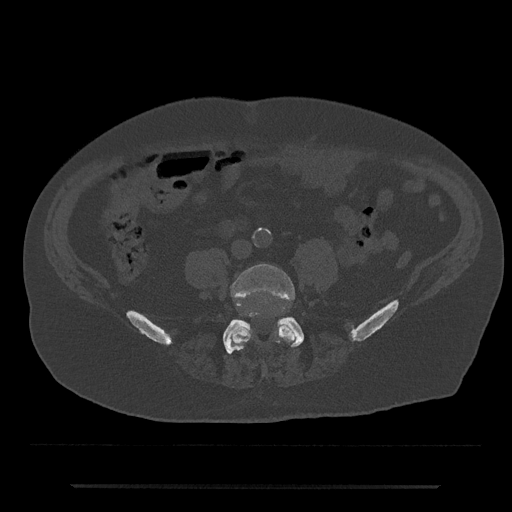
CT including the spine, one axial slice; position 319 of 797 along the scan axis; reconstruction kernel Br40s/3; bone window (W 1800 / L 400 HU); 0.5 mm slice thickness; 512 × 512 image matrix, field of view 434 × 434 mm. Male patient, age 80 years. From the clinical record (not read from this slice): primary cancer: prostate; vertebrae with lytic lesions (as recorded): L1, T11.
Annotated regions visible in this slice (semi-automatic segmentation, software-assisted and operator-edited):
- L4 vertebra: bounding box [x1, y1, x2, y2] px = [229, 264, 296, 349]
- L5 vertebra: [223, 312, 304, 354]